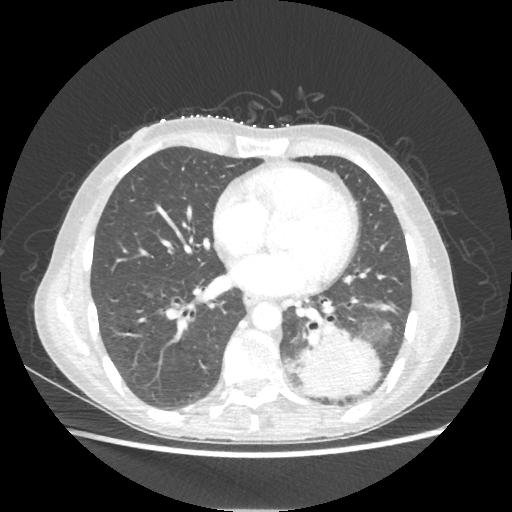
Chest CT, one axial slice; slice 93 of 221 in the series (ordered by position); lung window (W 1500 / L -600 HU); 1.25 mm slice thickness; 512 × 512 image matrix. Female patient, age 53 years. From the clinical record (not read from this slice): clinical TNM (as recorded): T3 N0 M0.
Structures marked on this image (bounding box drawn by a radiologist):
- lung tumour (recorded histology: adenocarcinoma): bounding box (x1, y1, x2, y2) in pixels: (293, 323, 380, 398)